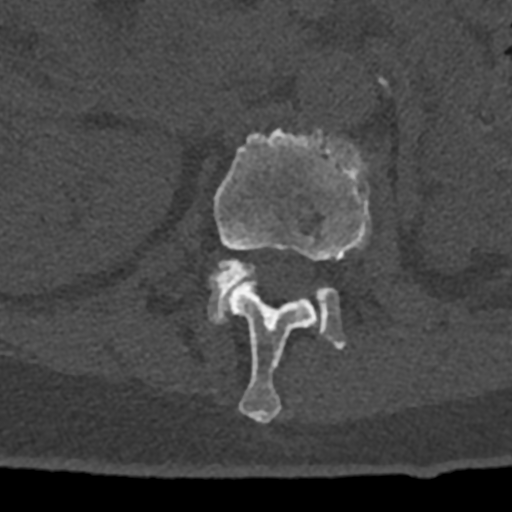
CT including the spine, one axial slice. Position 418 of 797 along the scan axis. Reconstruction kernel Br40s/3. Bone window (W 1800 / L 400 HU). 512 × 512 image matrix, field of view 160 × 160 mm. Male patient, age 74 years. Case-level facts recorded for this patient, not image findings: primary cancer: renal; vertebrae with lytic lesions (as recorded): T10, L1, L2, L3, L4, L5.
Annotated regions visible in this slice (semi-automatically segmented with operator editing):
- L1 vertebra: bounding box <213,123,372,424> (left, top, right, bottom; pixels)
- L2 vertebra: <208,260,346,349>